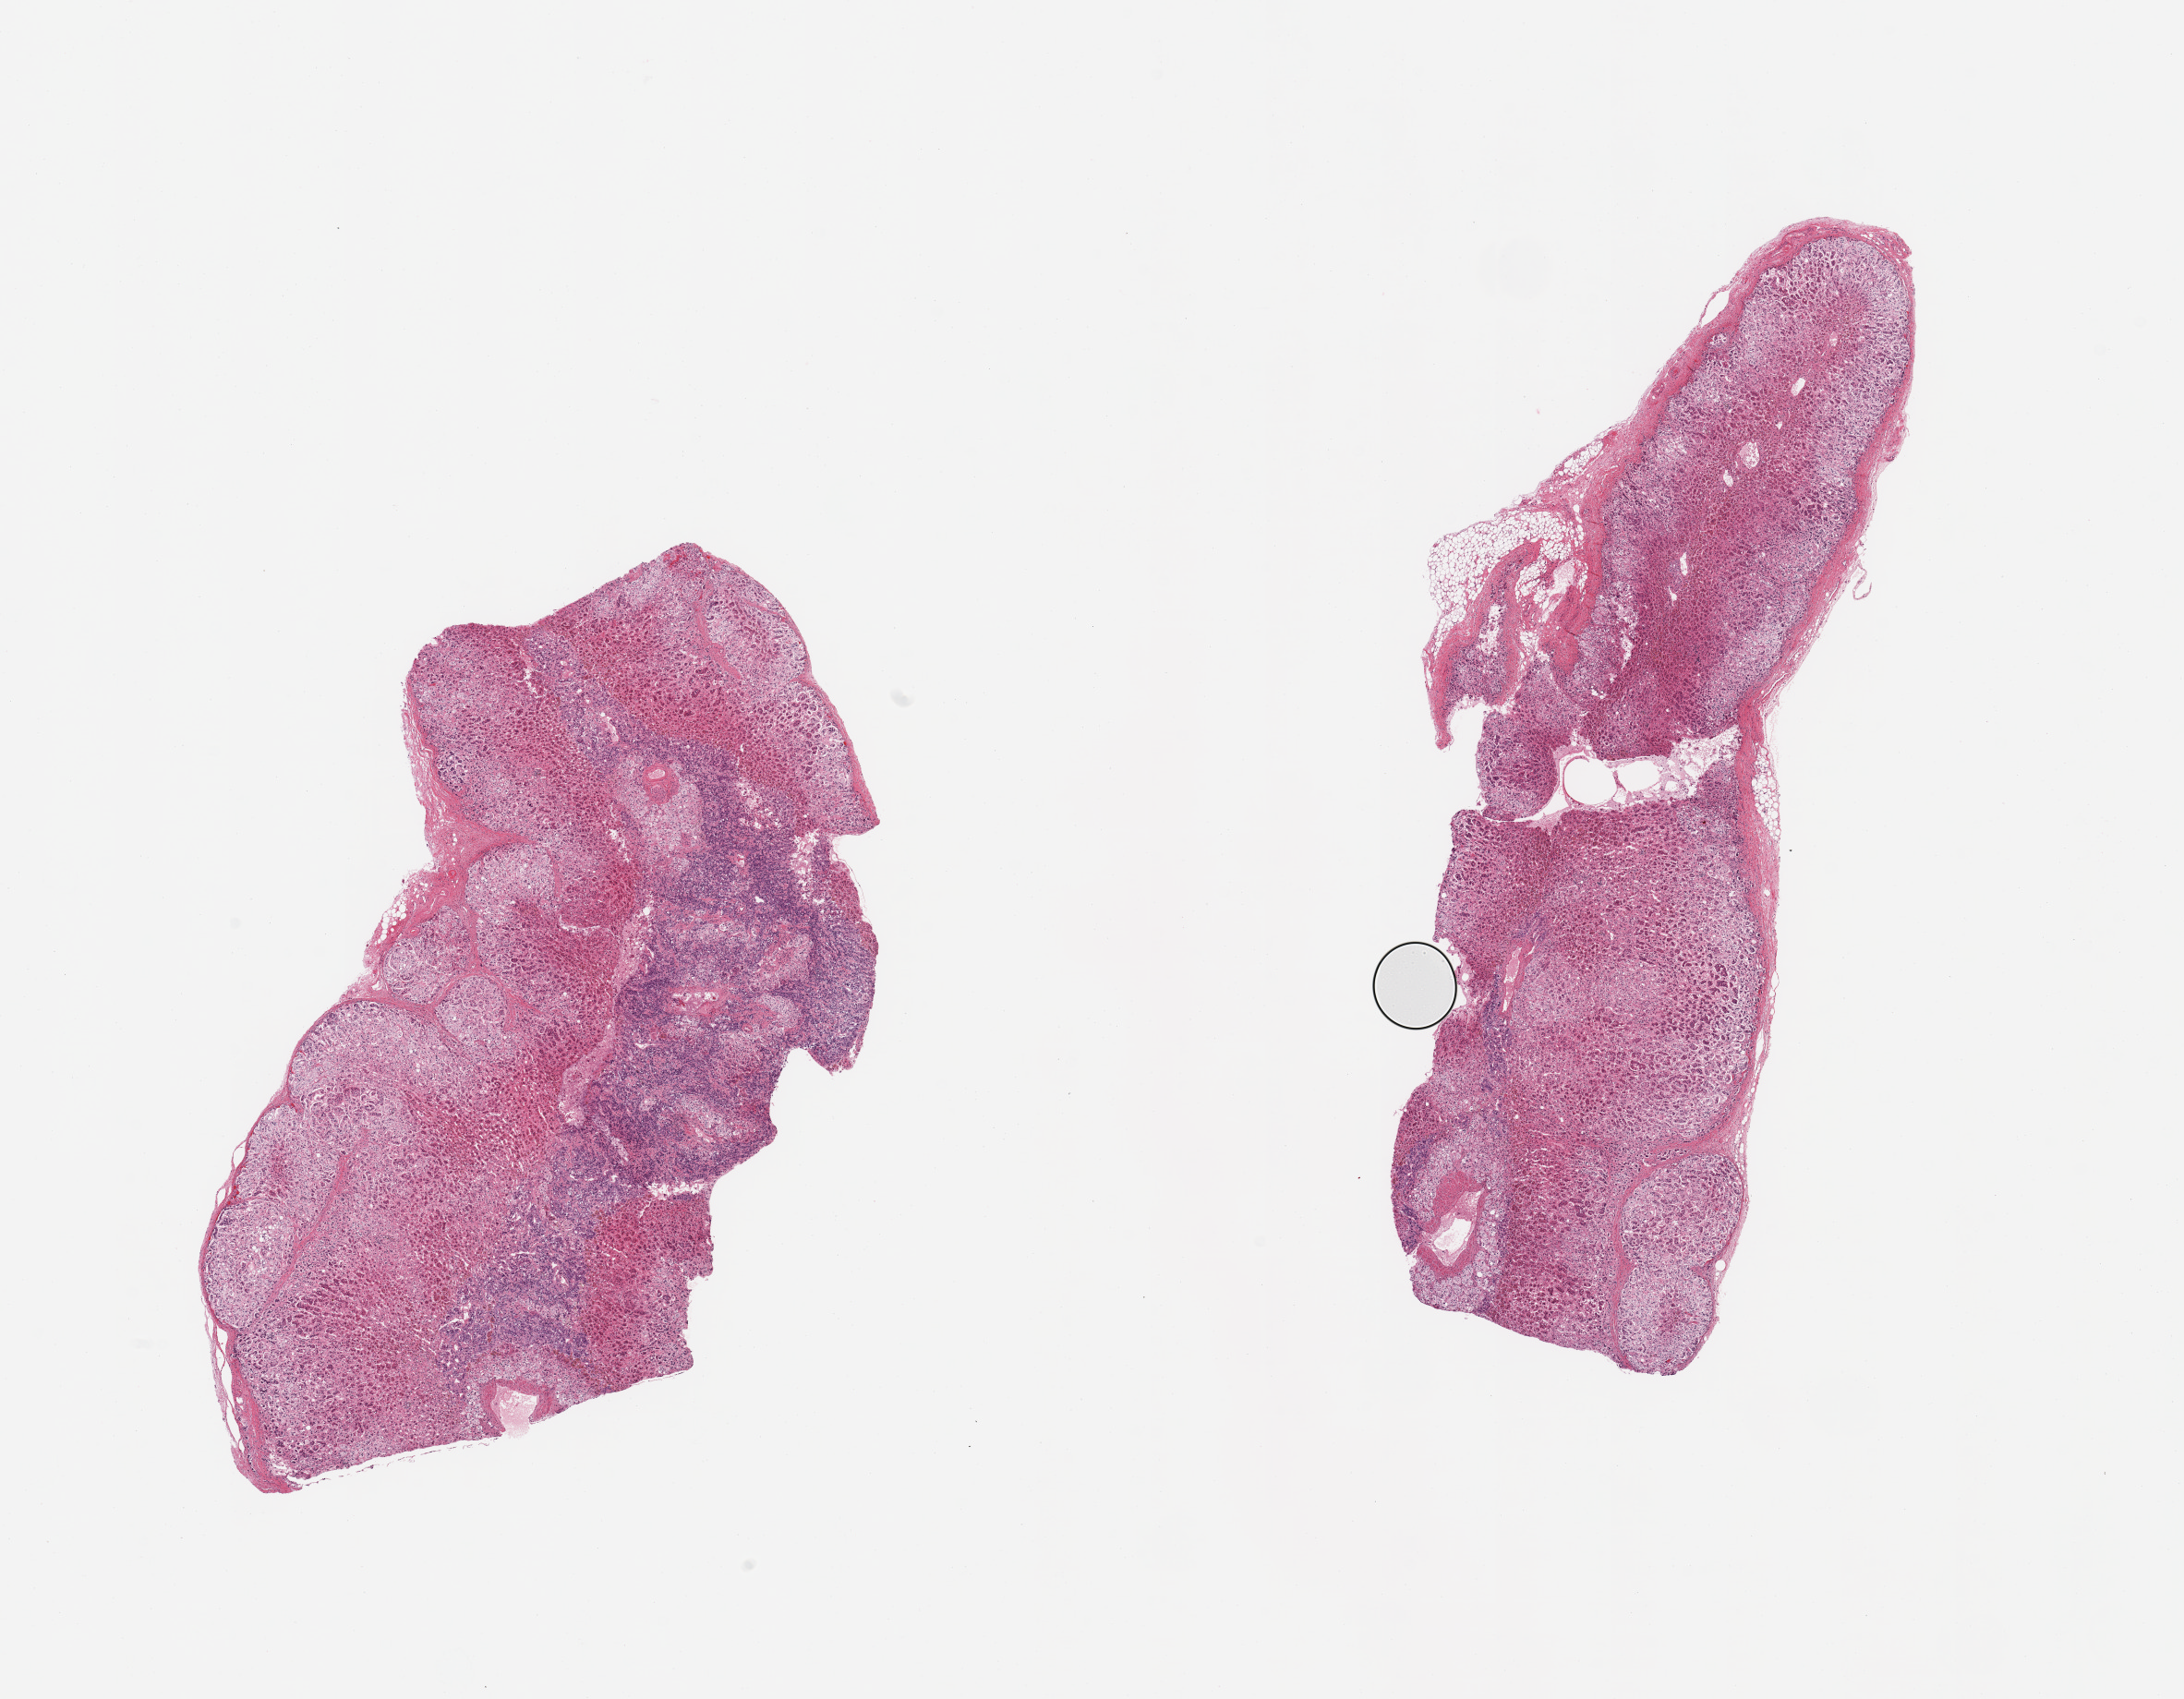
Digitized H&E-stained section, a low-resolution overview of the entire scanned area, about 18.7 x 14.6 mm (acquisition: 20x scan). PAXgene-fixed, paraffin-embedded tissue. Sampled site (target tissue): adrenal gland. Tissue donor sample. Male donor.
* review note (as recorded): 2 pieces; well trimmed, <5% fat content